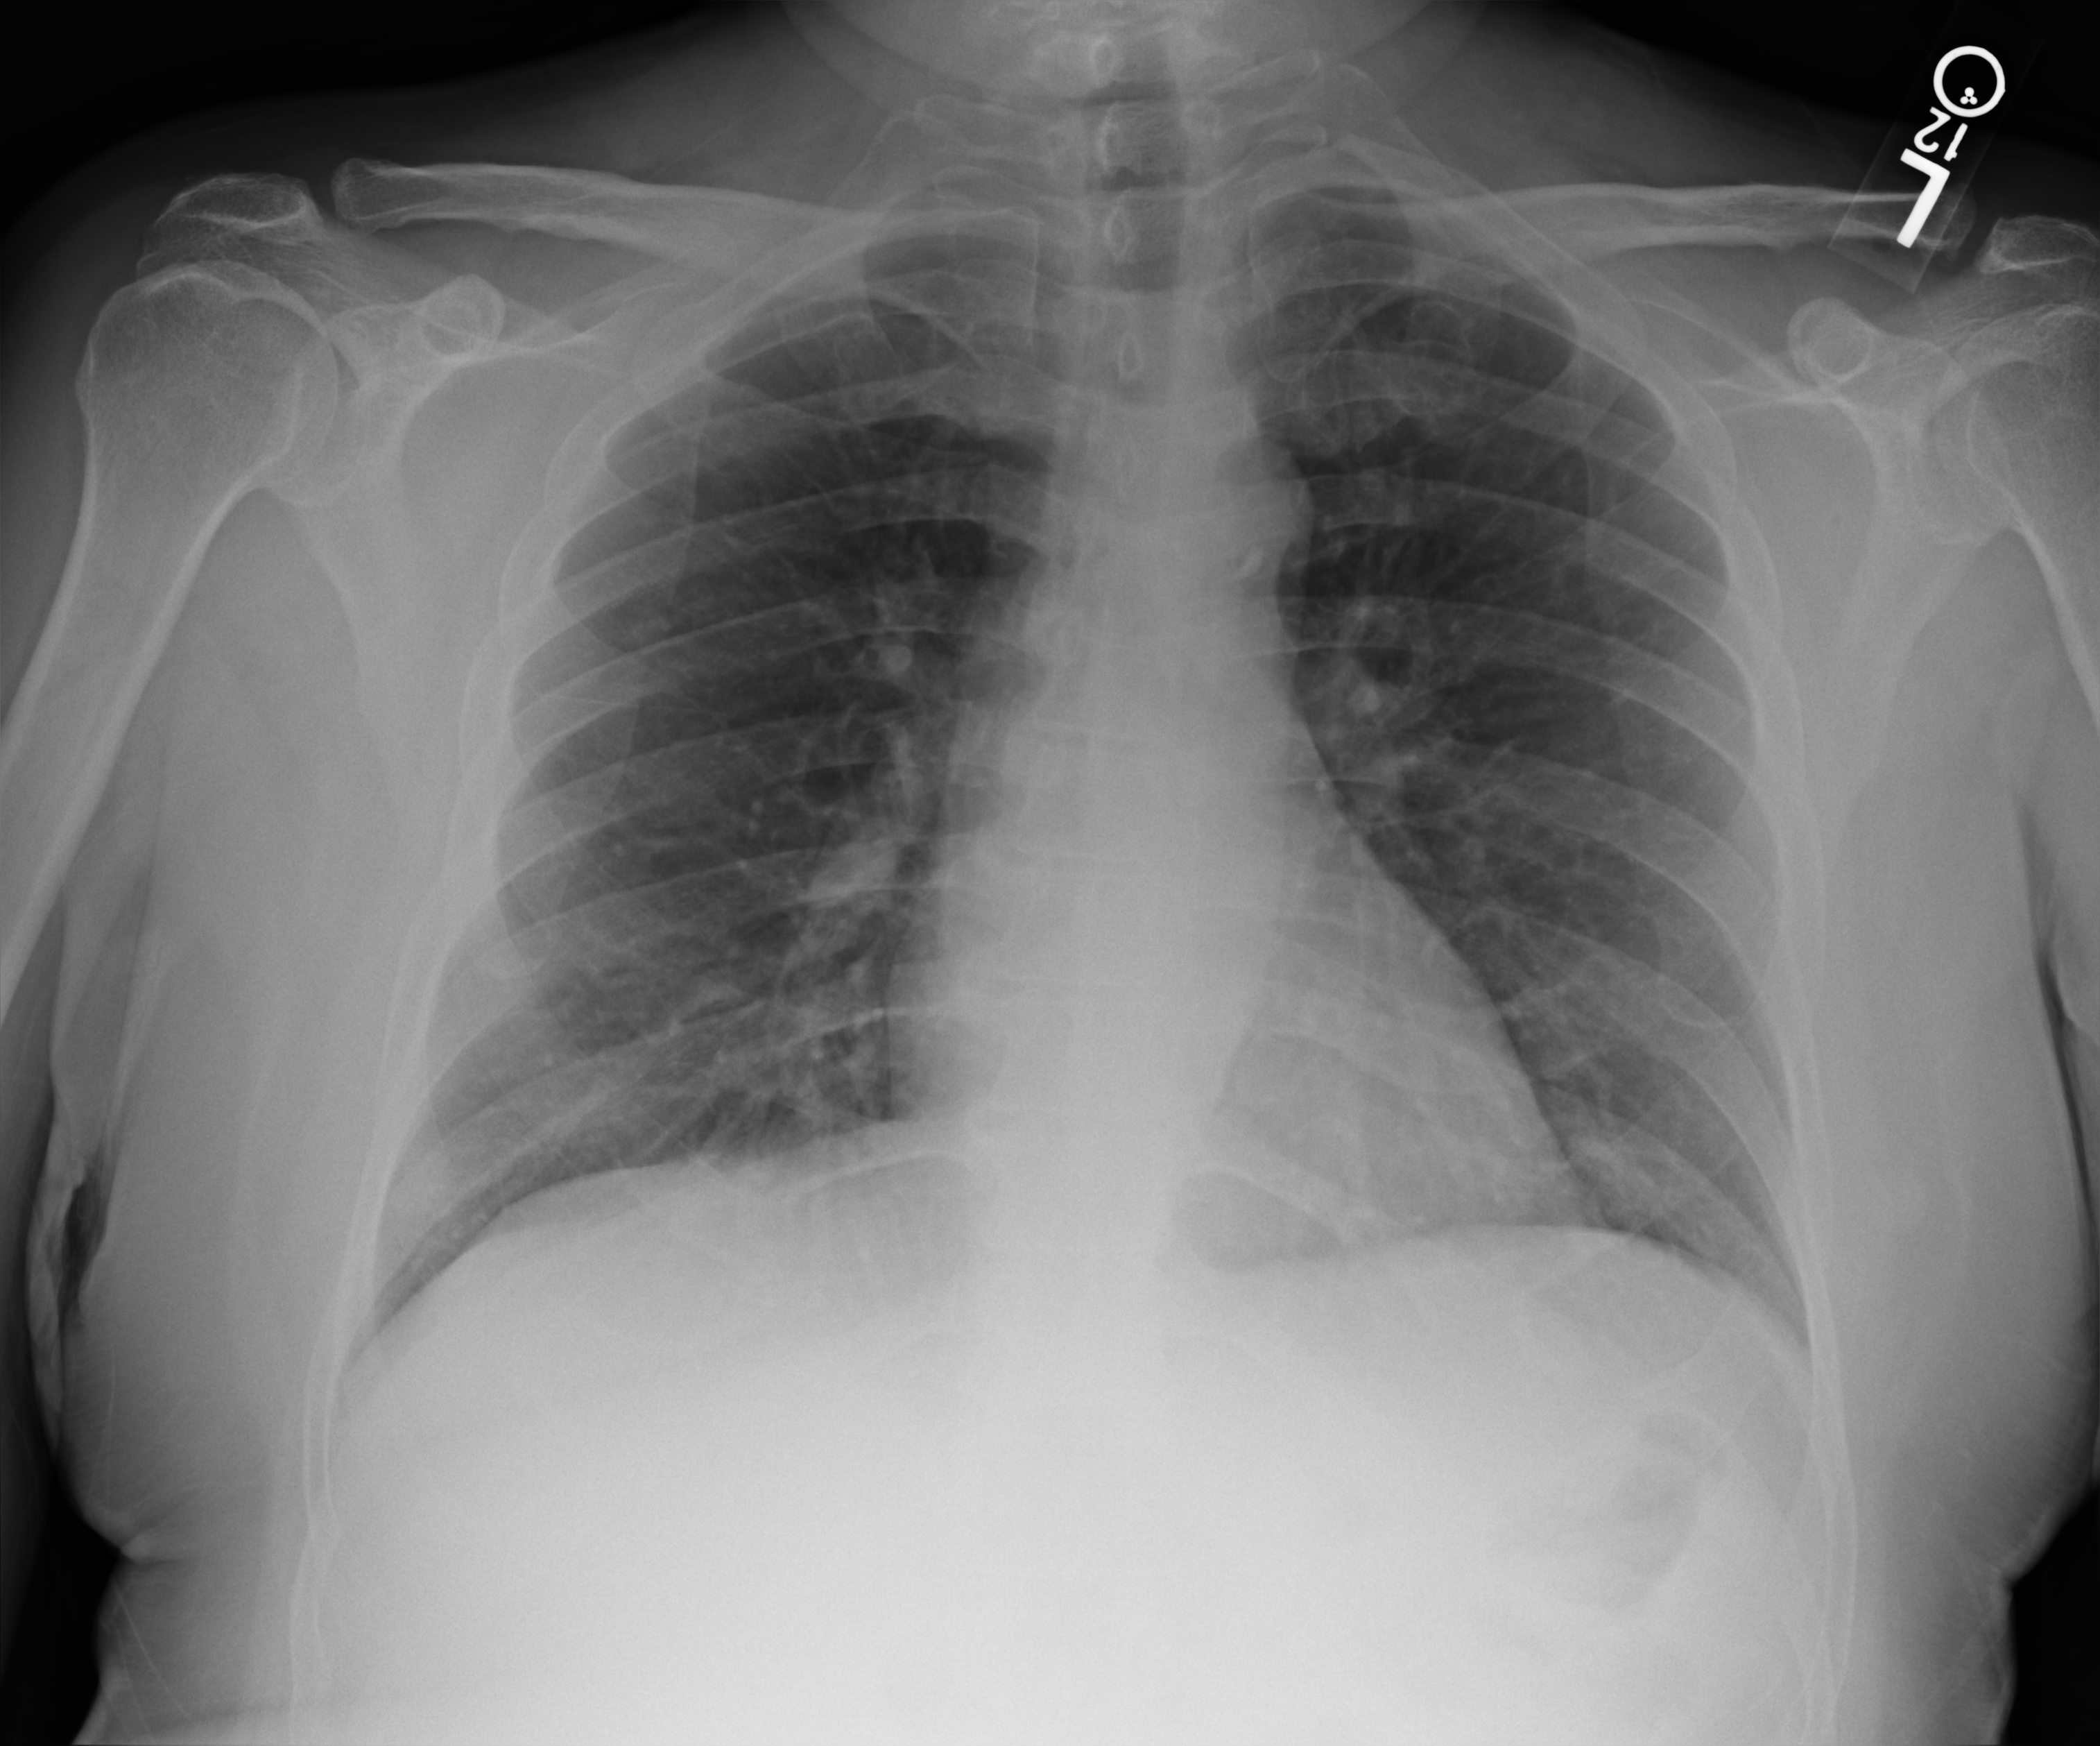
Chest X-ray (portable); anteroposterior (AP) projection. Patient hospitalised with COVID-19; male, aged 60–74 years.
Hospital-stay facts (about this admission, not read from this image; timing relative to this image not recorded): COPD (admission record): no; mechanically ventilated during this hospital stay: no.